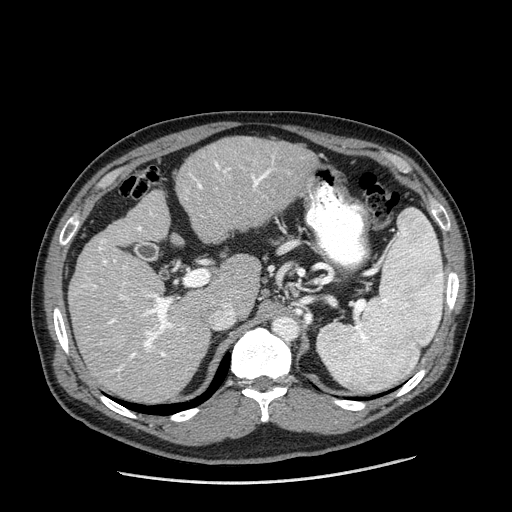
Contrast-enhanced abdominal CT (liver protocol), one axial slice. Position 115 of 198 along the scan axis. Reconstruction kernel STANDARD. 120 kVp. One of 2 acquisitions stored at this slice position. Soft-tissue window (W 400 / L 40 HU). 2.5 mm slice thickness. 512 × 512 image matrix, field of view 400 × 400 mm. From the clinical record (not read from this slice): diagnosis: hepatocellular carcinoma (patient treated with transarterial chemoembolisation; whether this scan precedes or follows treatment is not stated here); TNM stage (as recorded): Stage-II; Child-Pugh class: A.
Annotated regions visible in this slice (semi-automatically segmented with operator editing):
- liver parenchyma outside the tumour (the mass and vessels are separate outlines, so this box may not span the whole liver): box from (x=68, y=136) to (x=316, y=402) px
- liver vessels: (x=82, y=162)–(x=272, y=371)